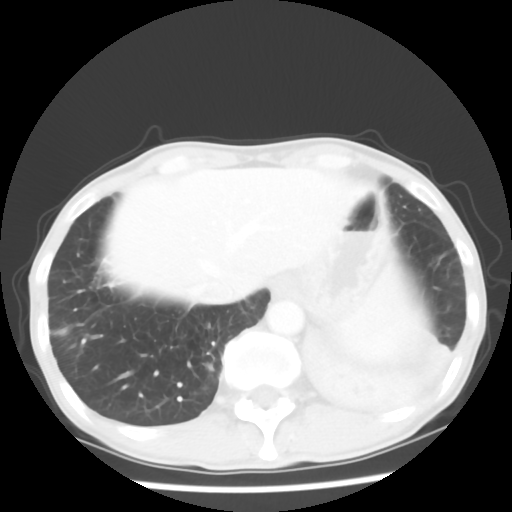
Chest CT, one axial slice; slice 9 of 64 in the series (ordered by position); reconstruction kernel STANDARD; lung window (W 1500 / L -600 HU); 5 mm slice thickness; 512 × 512 image matrix, field of view 313 × 313 mm. Patient: male, 68 years. From the clinical record (not read from this slice): clinical TNM (as recorded): T4 N0 M0.
Annotated regions visible in this slice (bounding box drawn by a radiologist):
- lung tumour (recorded histology: squamous cell carcinoma): bounding box [x1, y1, x2, y2] px = [292, 323, 457, 427]